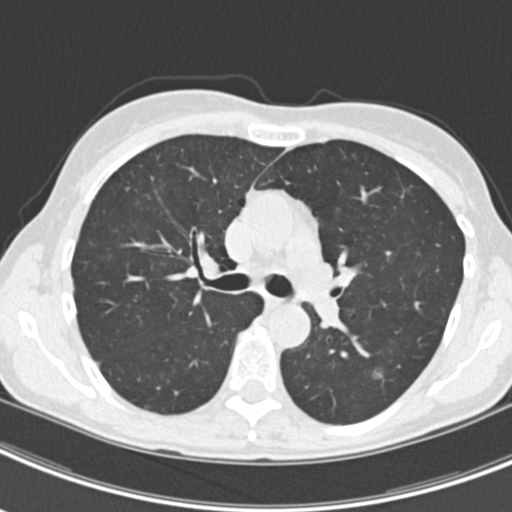
Low-dose screening chest CT, axial slice. Second screening round (one year after baseline). Lung window (W 1500 / L -600 HU). 2 mm slice thickness. Standard (soft-tissue) reconstruction kernel (B30f). 512 × 512 image matrix. Female participant, aged 63 years at enrolment. Current smoker at enrolment.
Lesion marked by an expert reader, bounding box <364,355,406,392> (left, top, right, bottom; pixels). The screening reader recorded 9 non-calcified nodules or masses ≥4 mm on this exam (left upper lobe, right upper lobe, left upper lobe, left lower lobe, right middle lobe, left lower lobe, left lower lobe, right lower lobe, right lower lobe); which of them this box marks is not recorded.